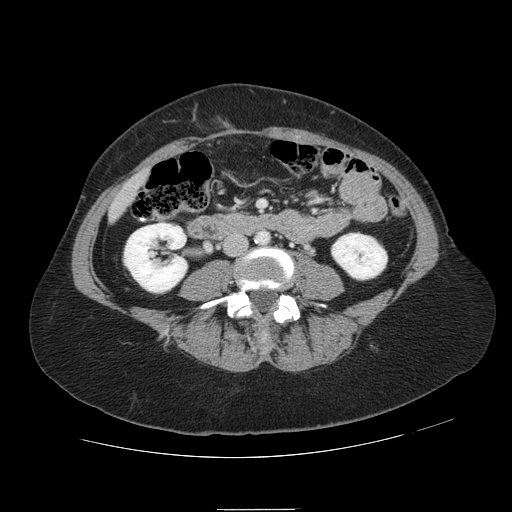
Contrast-enhanced abdominal CT, one axial slice; position 2 of 121 along the scan axis; 120 kVp; intravenous contrast given; soft-tissue window (W 400 / L 40 HU); 2.5 mm slice thickness; 512 × 512 image matrix, field of view 400 × 400 mm. Female patient, age 52 years. Case-level facts recorded for this patient, not image findings: diagnosis: colorectal cancer liver metastases, imaged before liver resection; multiple liver metastases: yes; largest metastasis: 6.3 cm; chemotherapy before resection: yes.
Outlined on this slice (manually delineated by an expert):
- liver: bounding box [x1, y1, x2, y2] px = [112, 174, 145, 216]